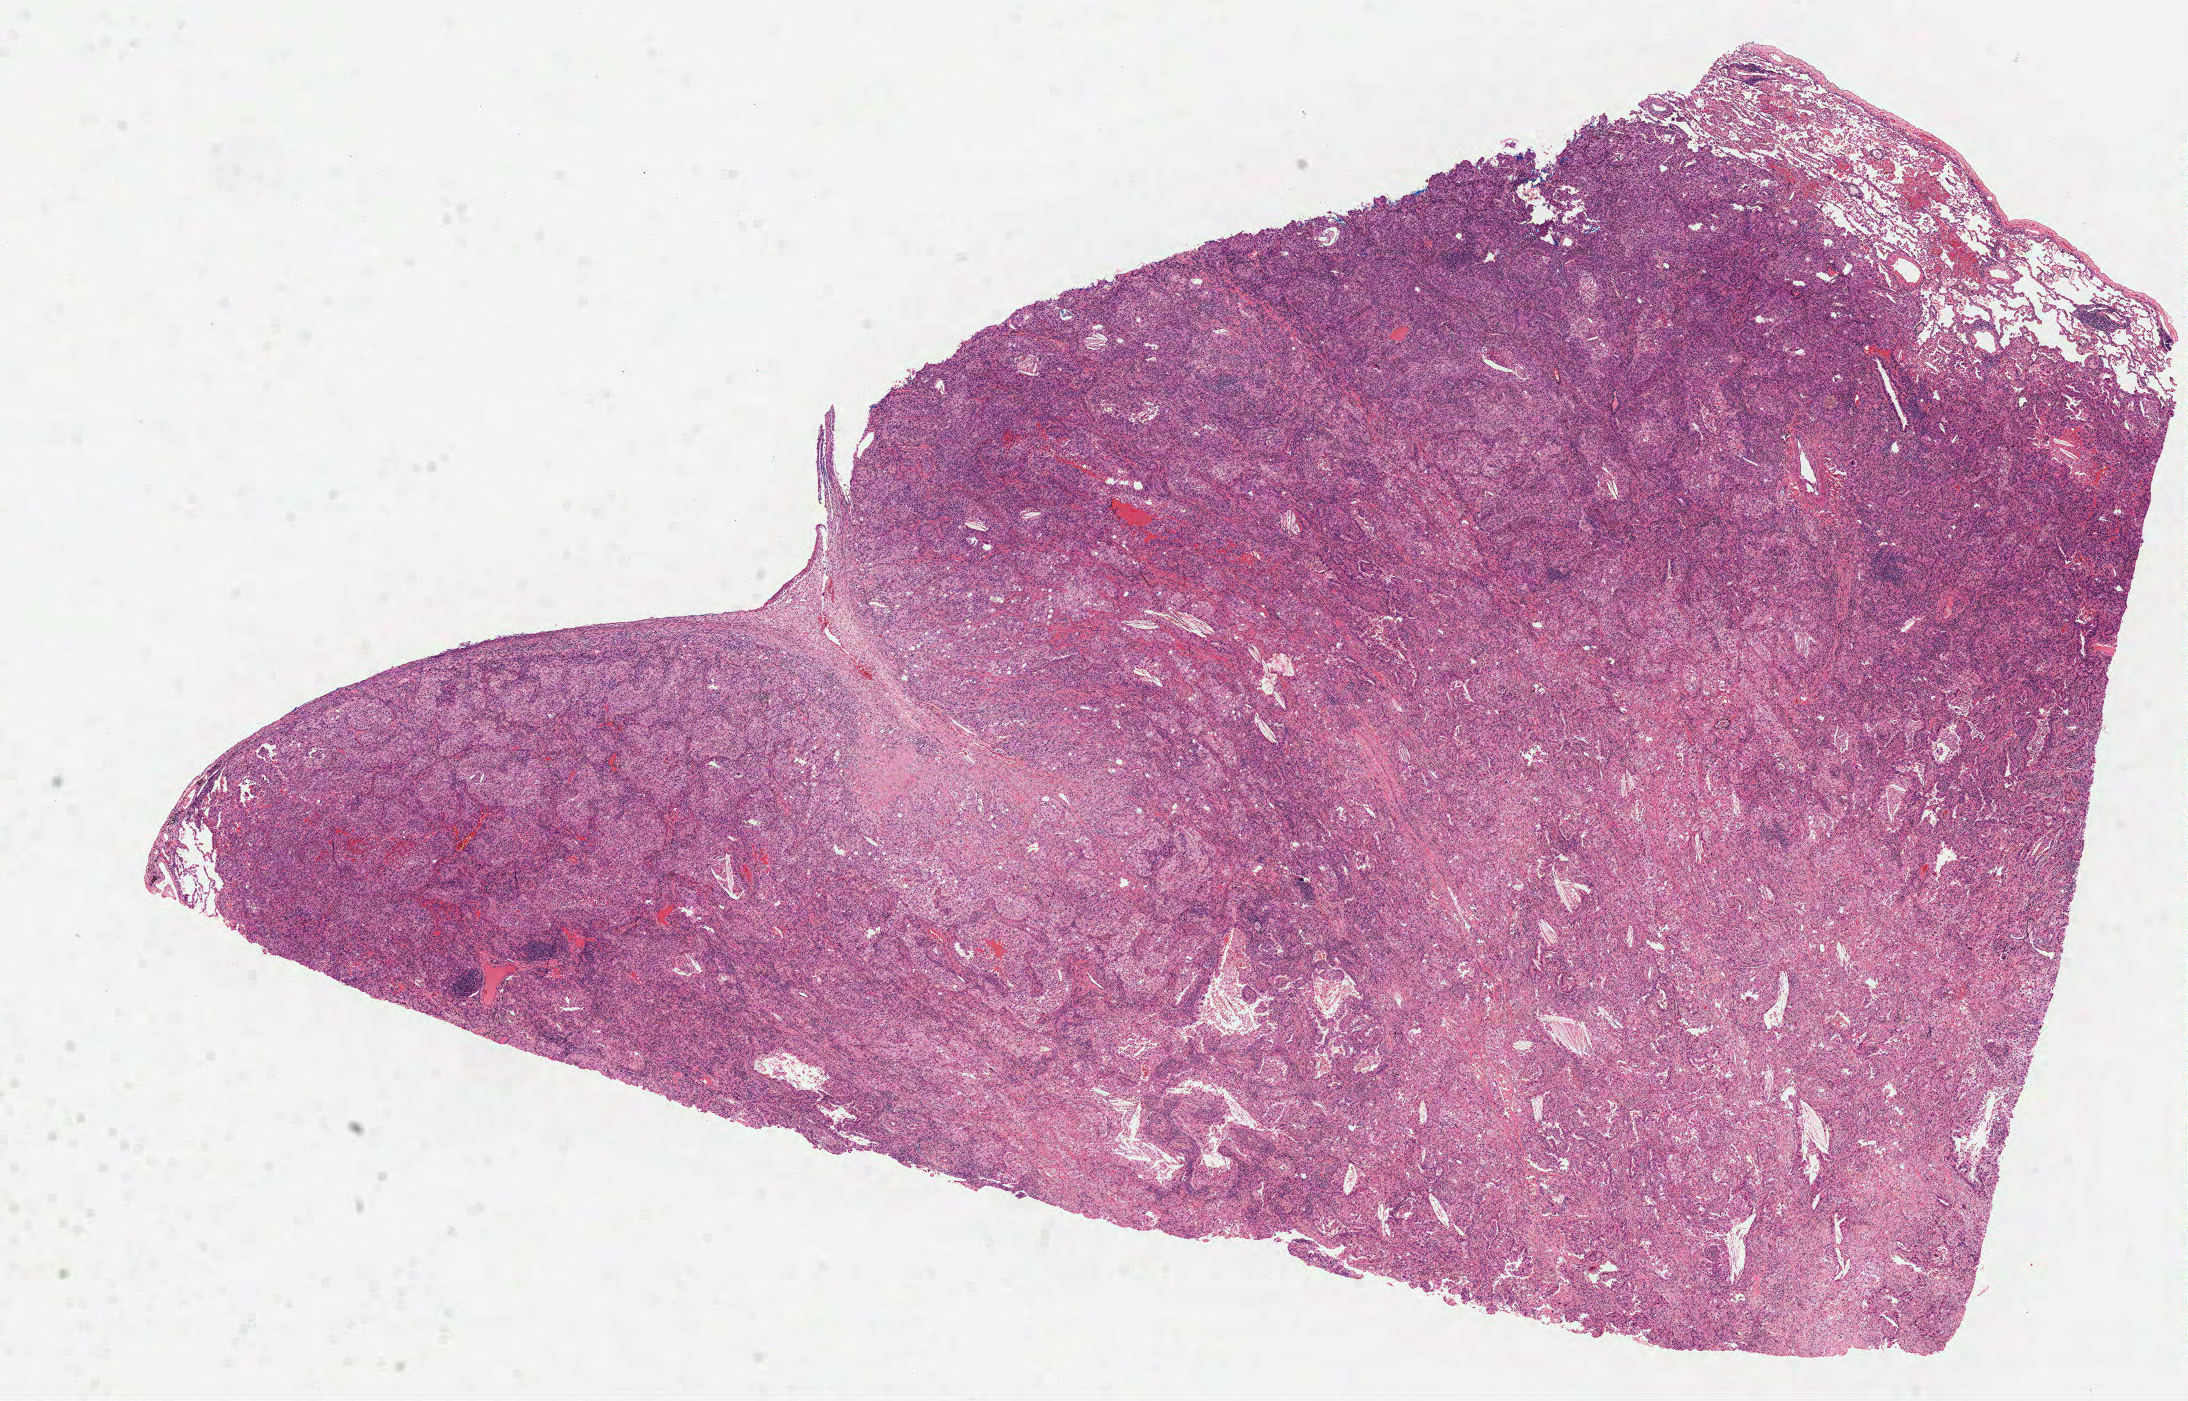
Hematoxylin and eosin (H&E) stained whole-slide image — whole scanned area (about 17.6 x 11.3 mm, acquisition: 40x scan) shown as a low-resolution overview. Formalin-fixed paraffin-embedded (FFPE) diagnostic section. Sample: primary tumour, lung. Female, age 54 years at initial diagnosis.
Diagnosis: Adenocarcinoma with mixed subtypes (upper lobe, lung). AJCC pathologic stage: IIIA (7th edition).